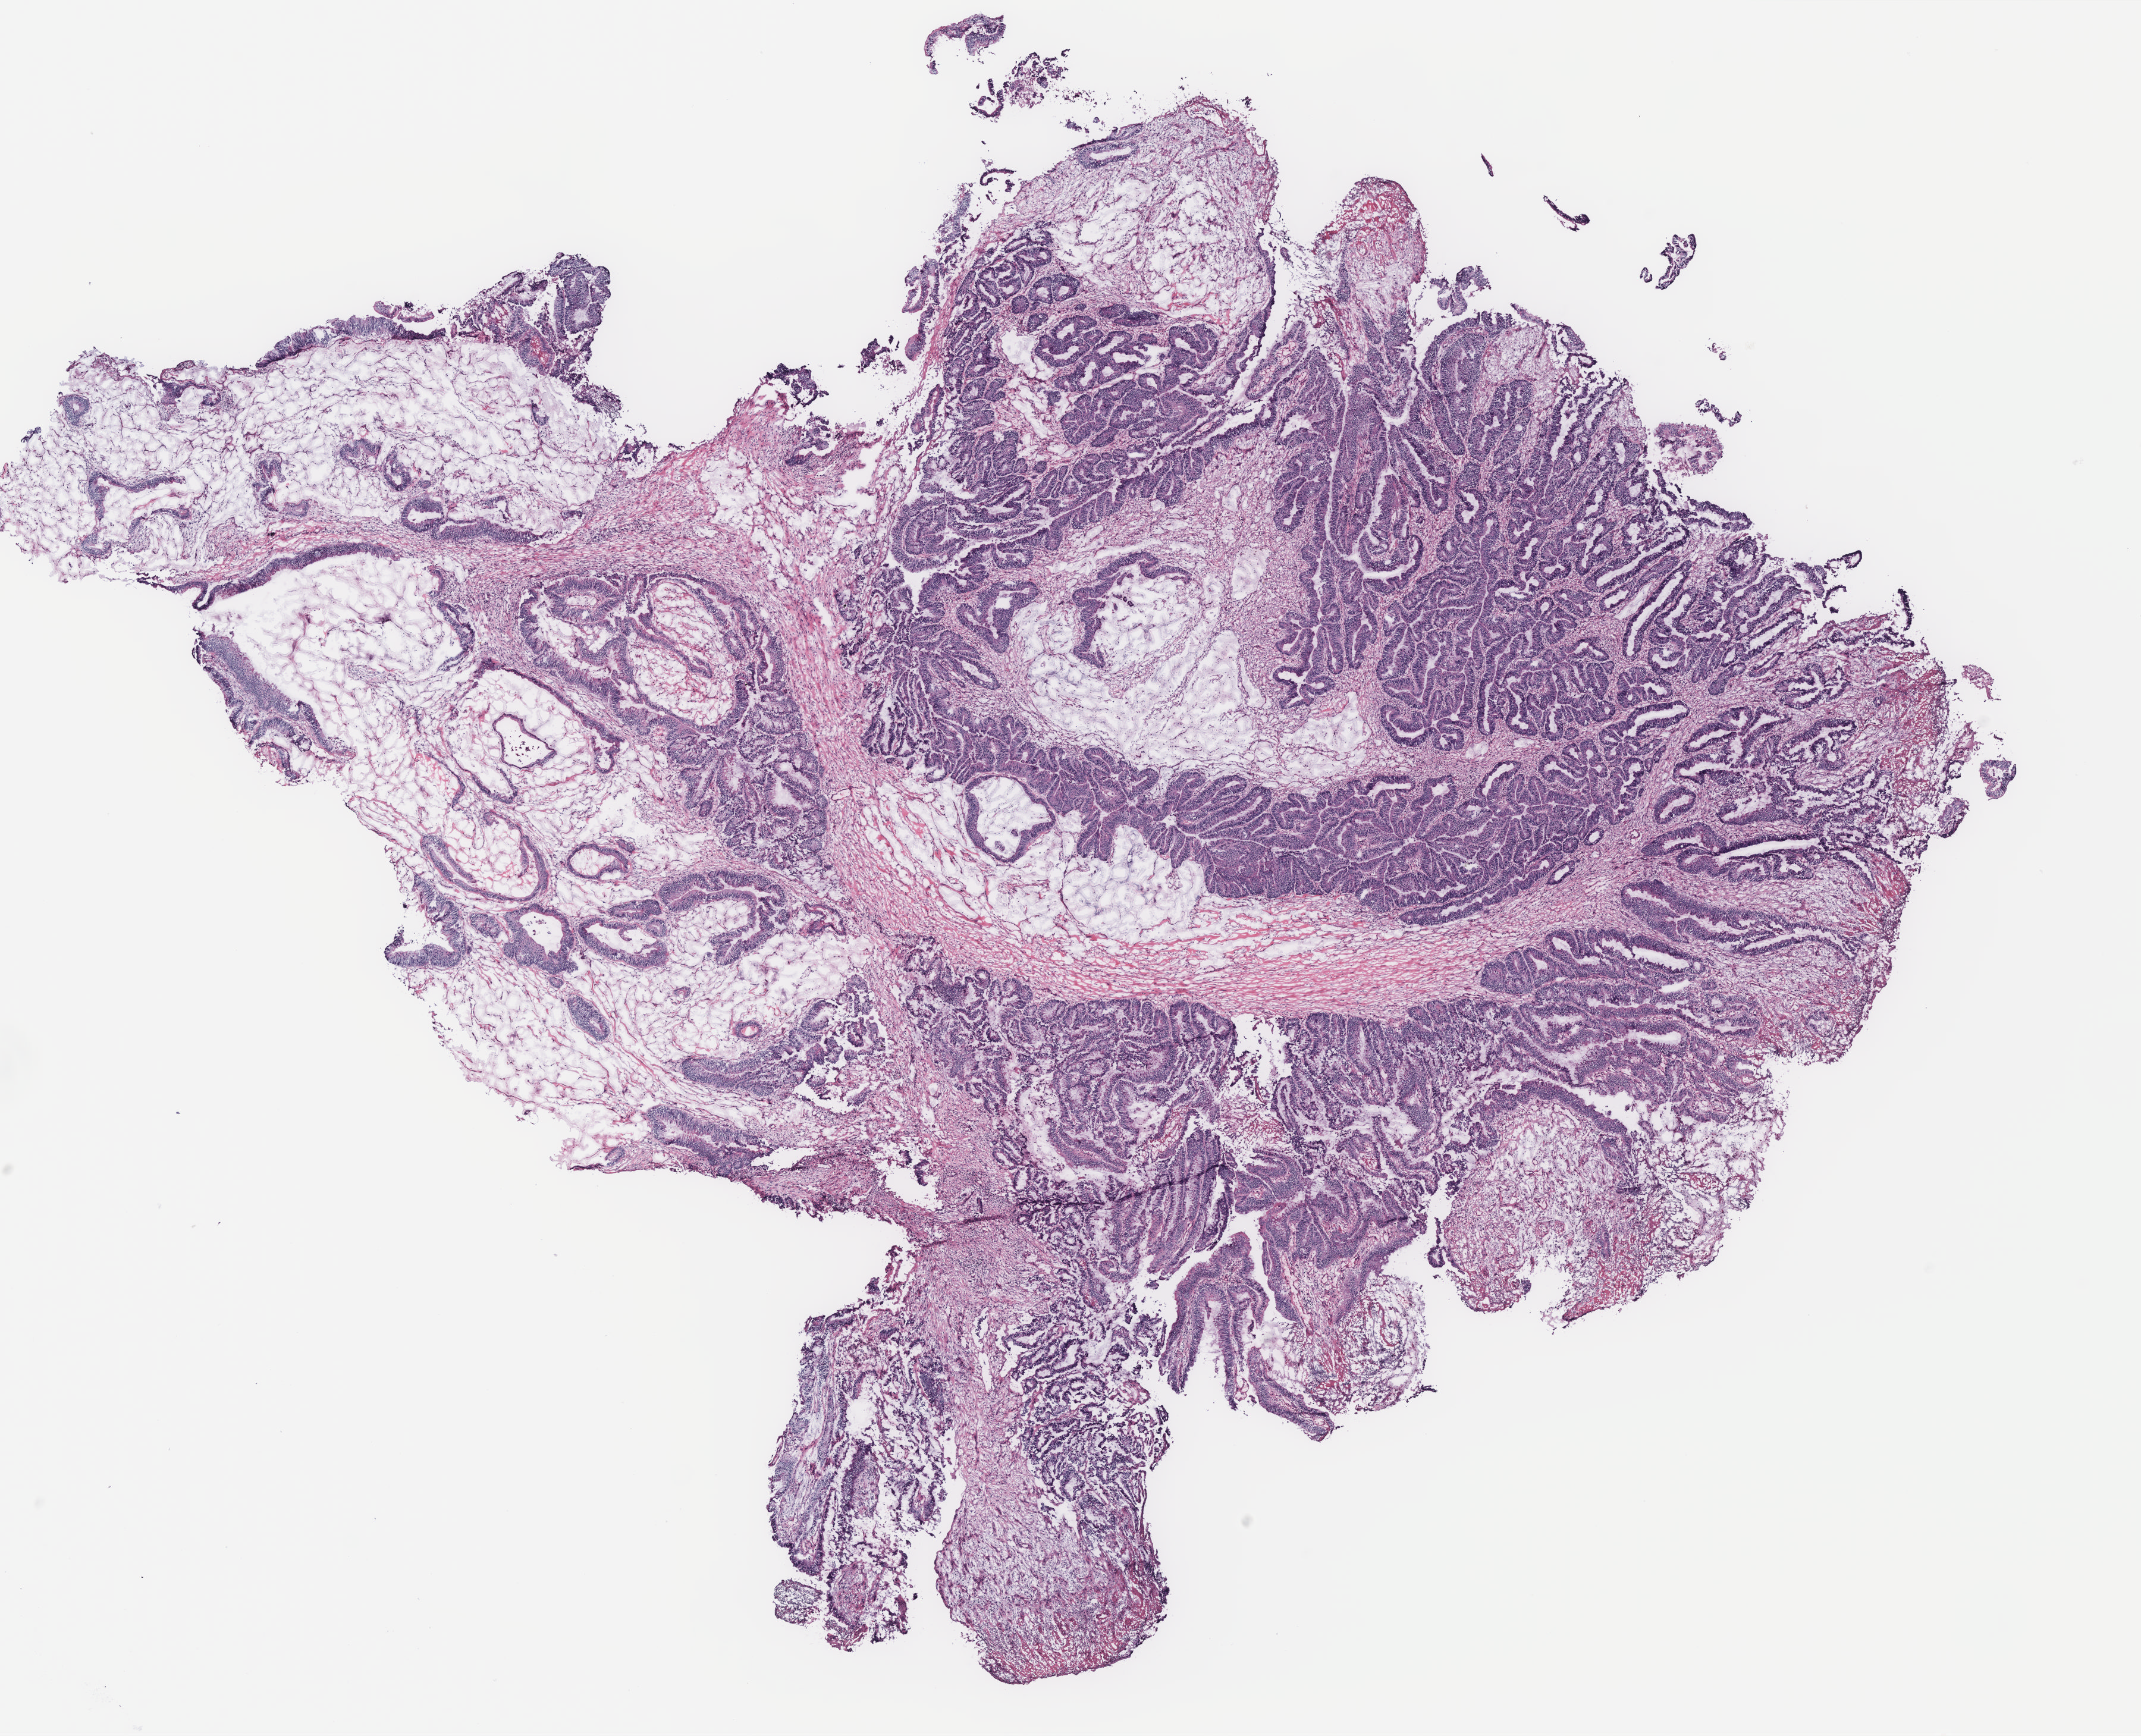
Hematoxylin and eosin (H&E) stained whole-slide image, a low-resolution overview of the entire scanned area, about 14.4 x 11.7 mm (from a 40x scan); colon, tissue type not recorded. Patient sex: female.
Patient diagnosis: Adenocarcinoma, NOS.